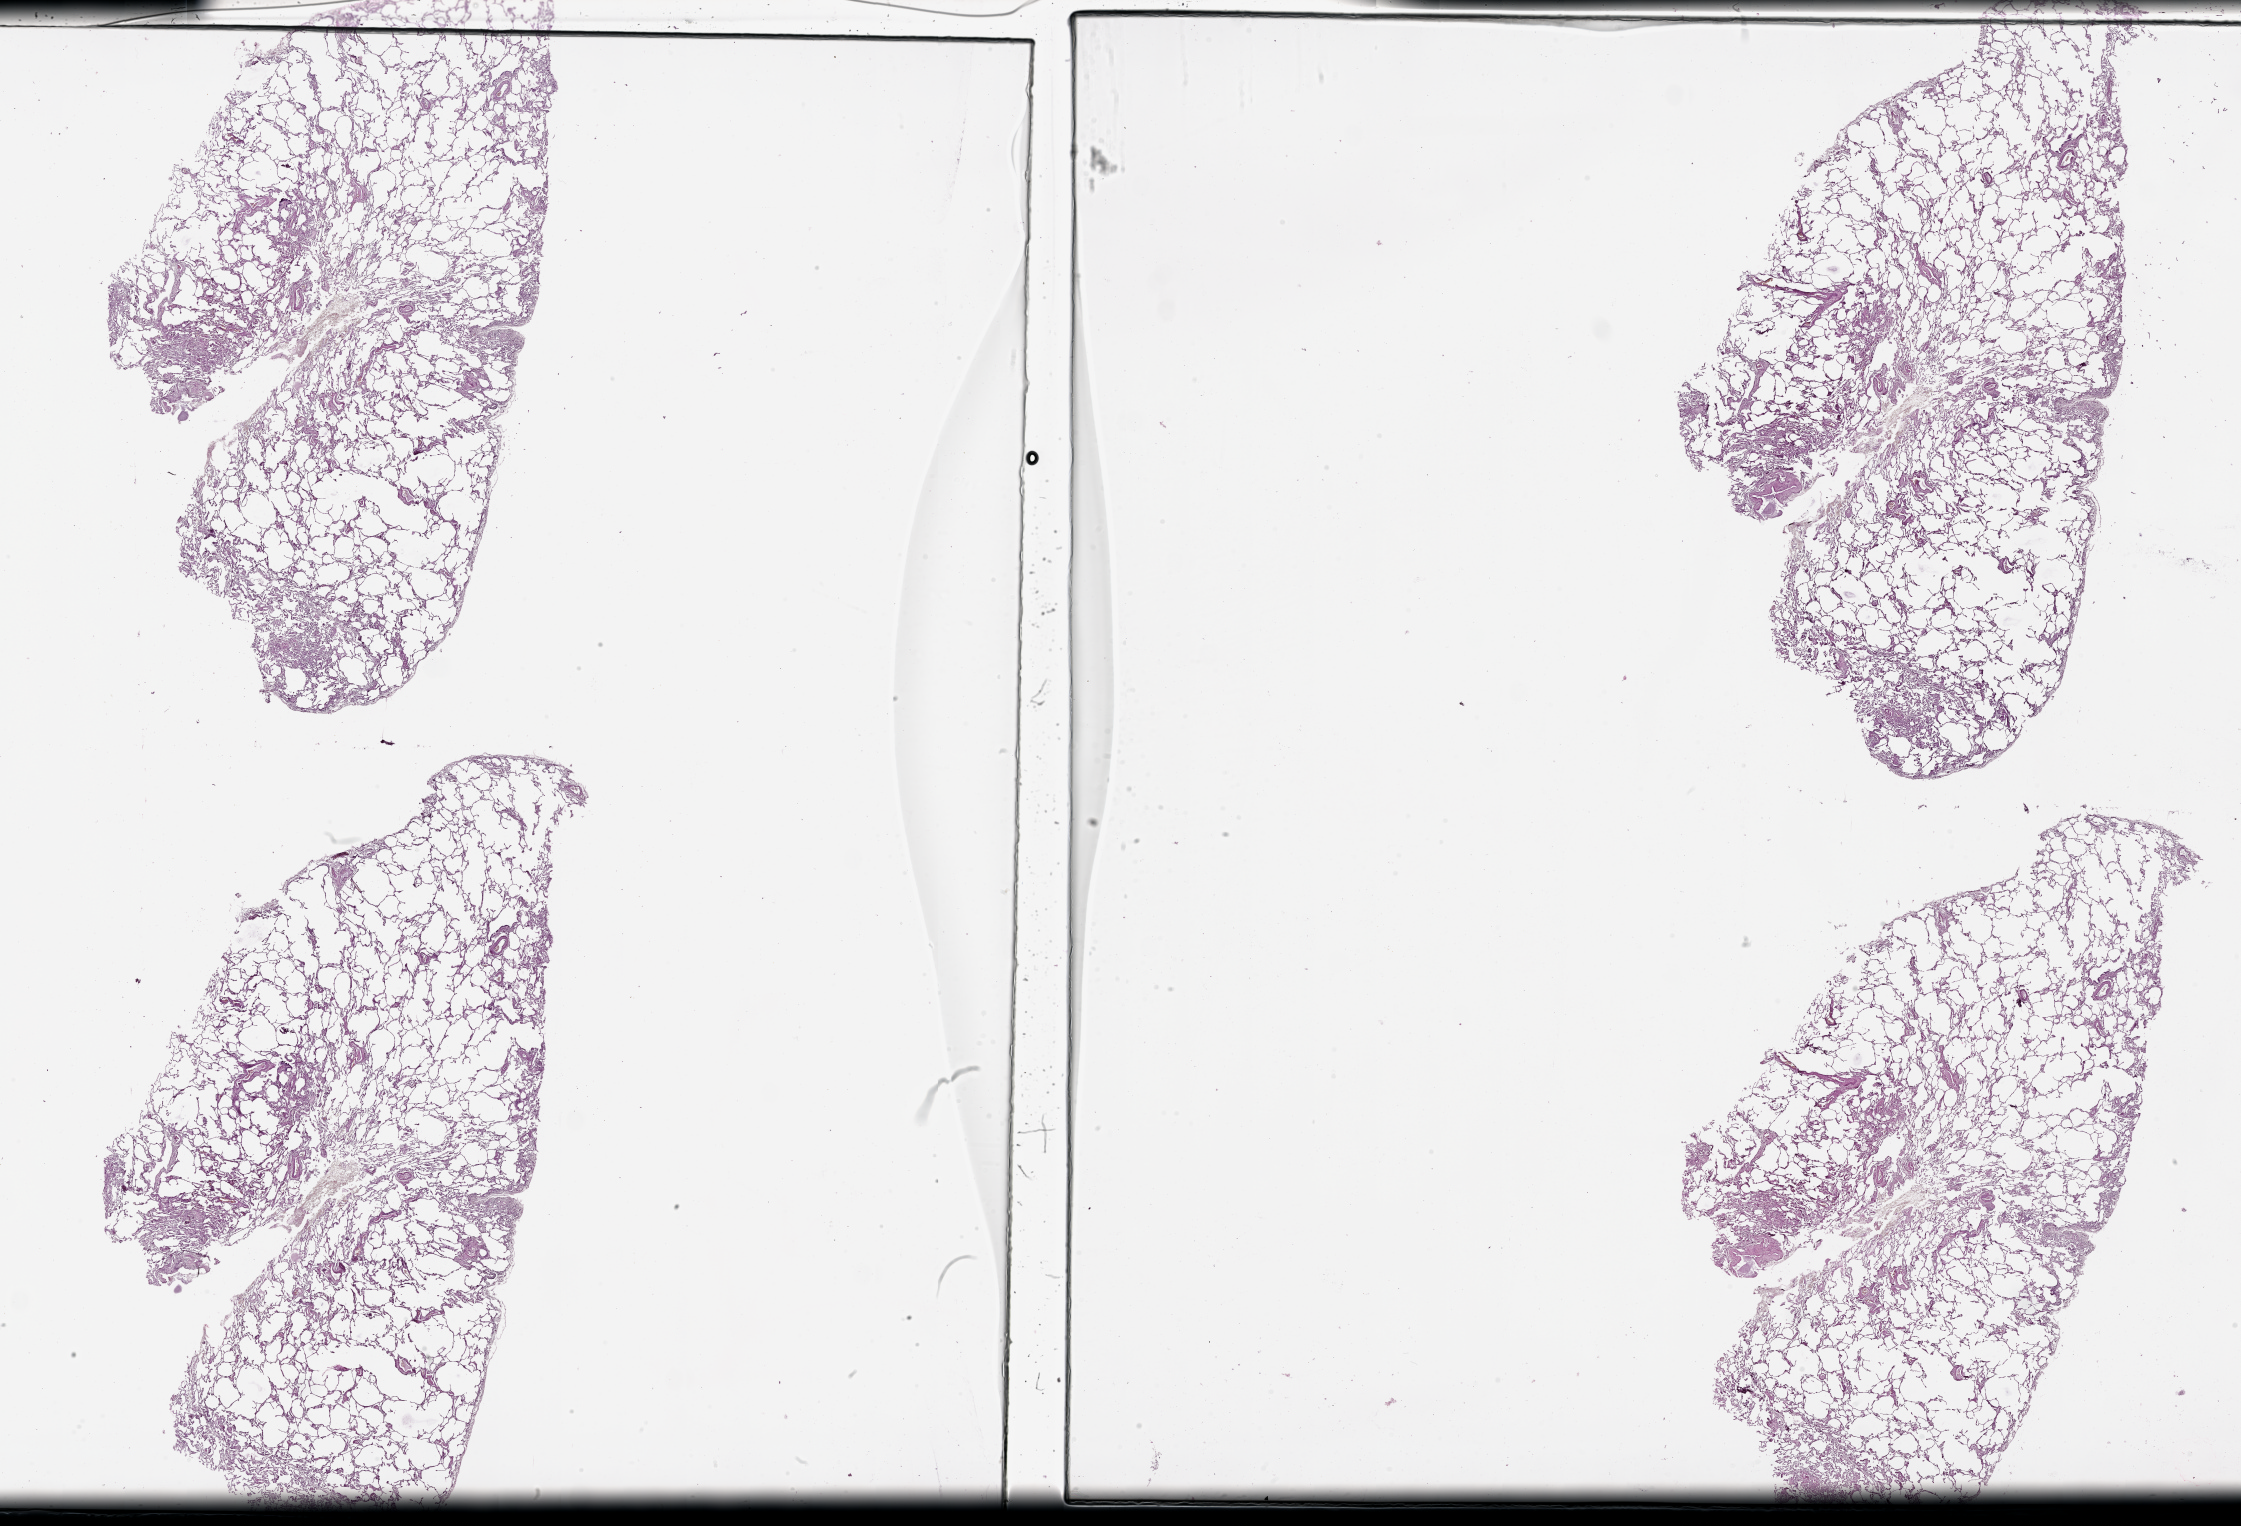
Whole-slide histology image, Hematoxylin and eosin (H&E) stained — shown as a low-resolution overview of the whole scanned area (about 36.1 x 24.6 mm); normal (non-tumour) tissue sample, lung. Female, 63 y/o.
This section: normal (non-tumour) tissue from the same patient. Patient diagnosis (cohort enrolment): squamous cell carcinoma (lung).